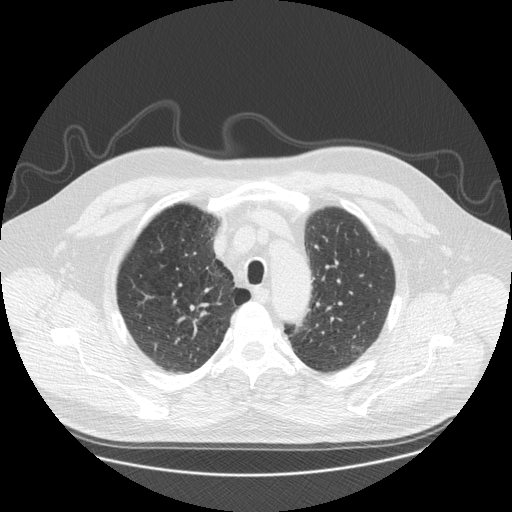
Axial slice from a low-dose chest CT screening exam. Third screening round (two years after baseline). Lung window (W 1500 / L -600 HU). Standard (soft-tissue) reconstruction kernel (STANDARD). Slice 33 of 173 in the series. 512 × 512 image matrix, field of view 400 × 400 mm. Male, age 61 years at enrolment. Former smoker at enrolment.
Expert-annotated lung lesion, bounding box [x1, y1, x2, y2] px = [169, 302, 216, 335]. Reader record for this screening exam (exam-level; its link to the box is not recorded): non-calcified nodule or mass ≥4 mm, right upper lobe, 10 × 7 mm, smooth margins, soft tissue attenuation, pre-existing on the prior screen: yes; interval growth: yes. Later outcome: lung cancer diagnosed 110 days after this screen — squamous cell carcinoma, NOS, right upper lobe, moderately differentiated (G2), stage IA (AJCC 6th edition), 10 mm at pathology.